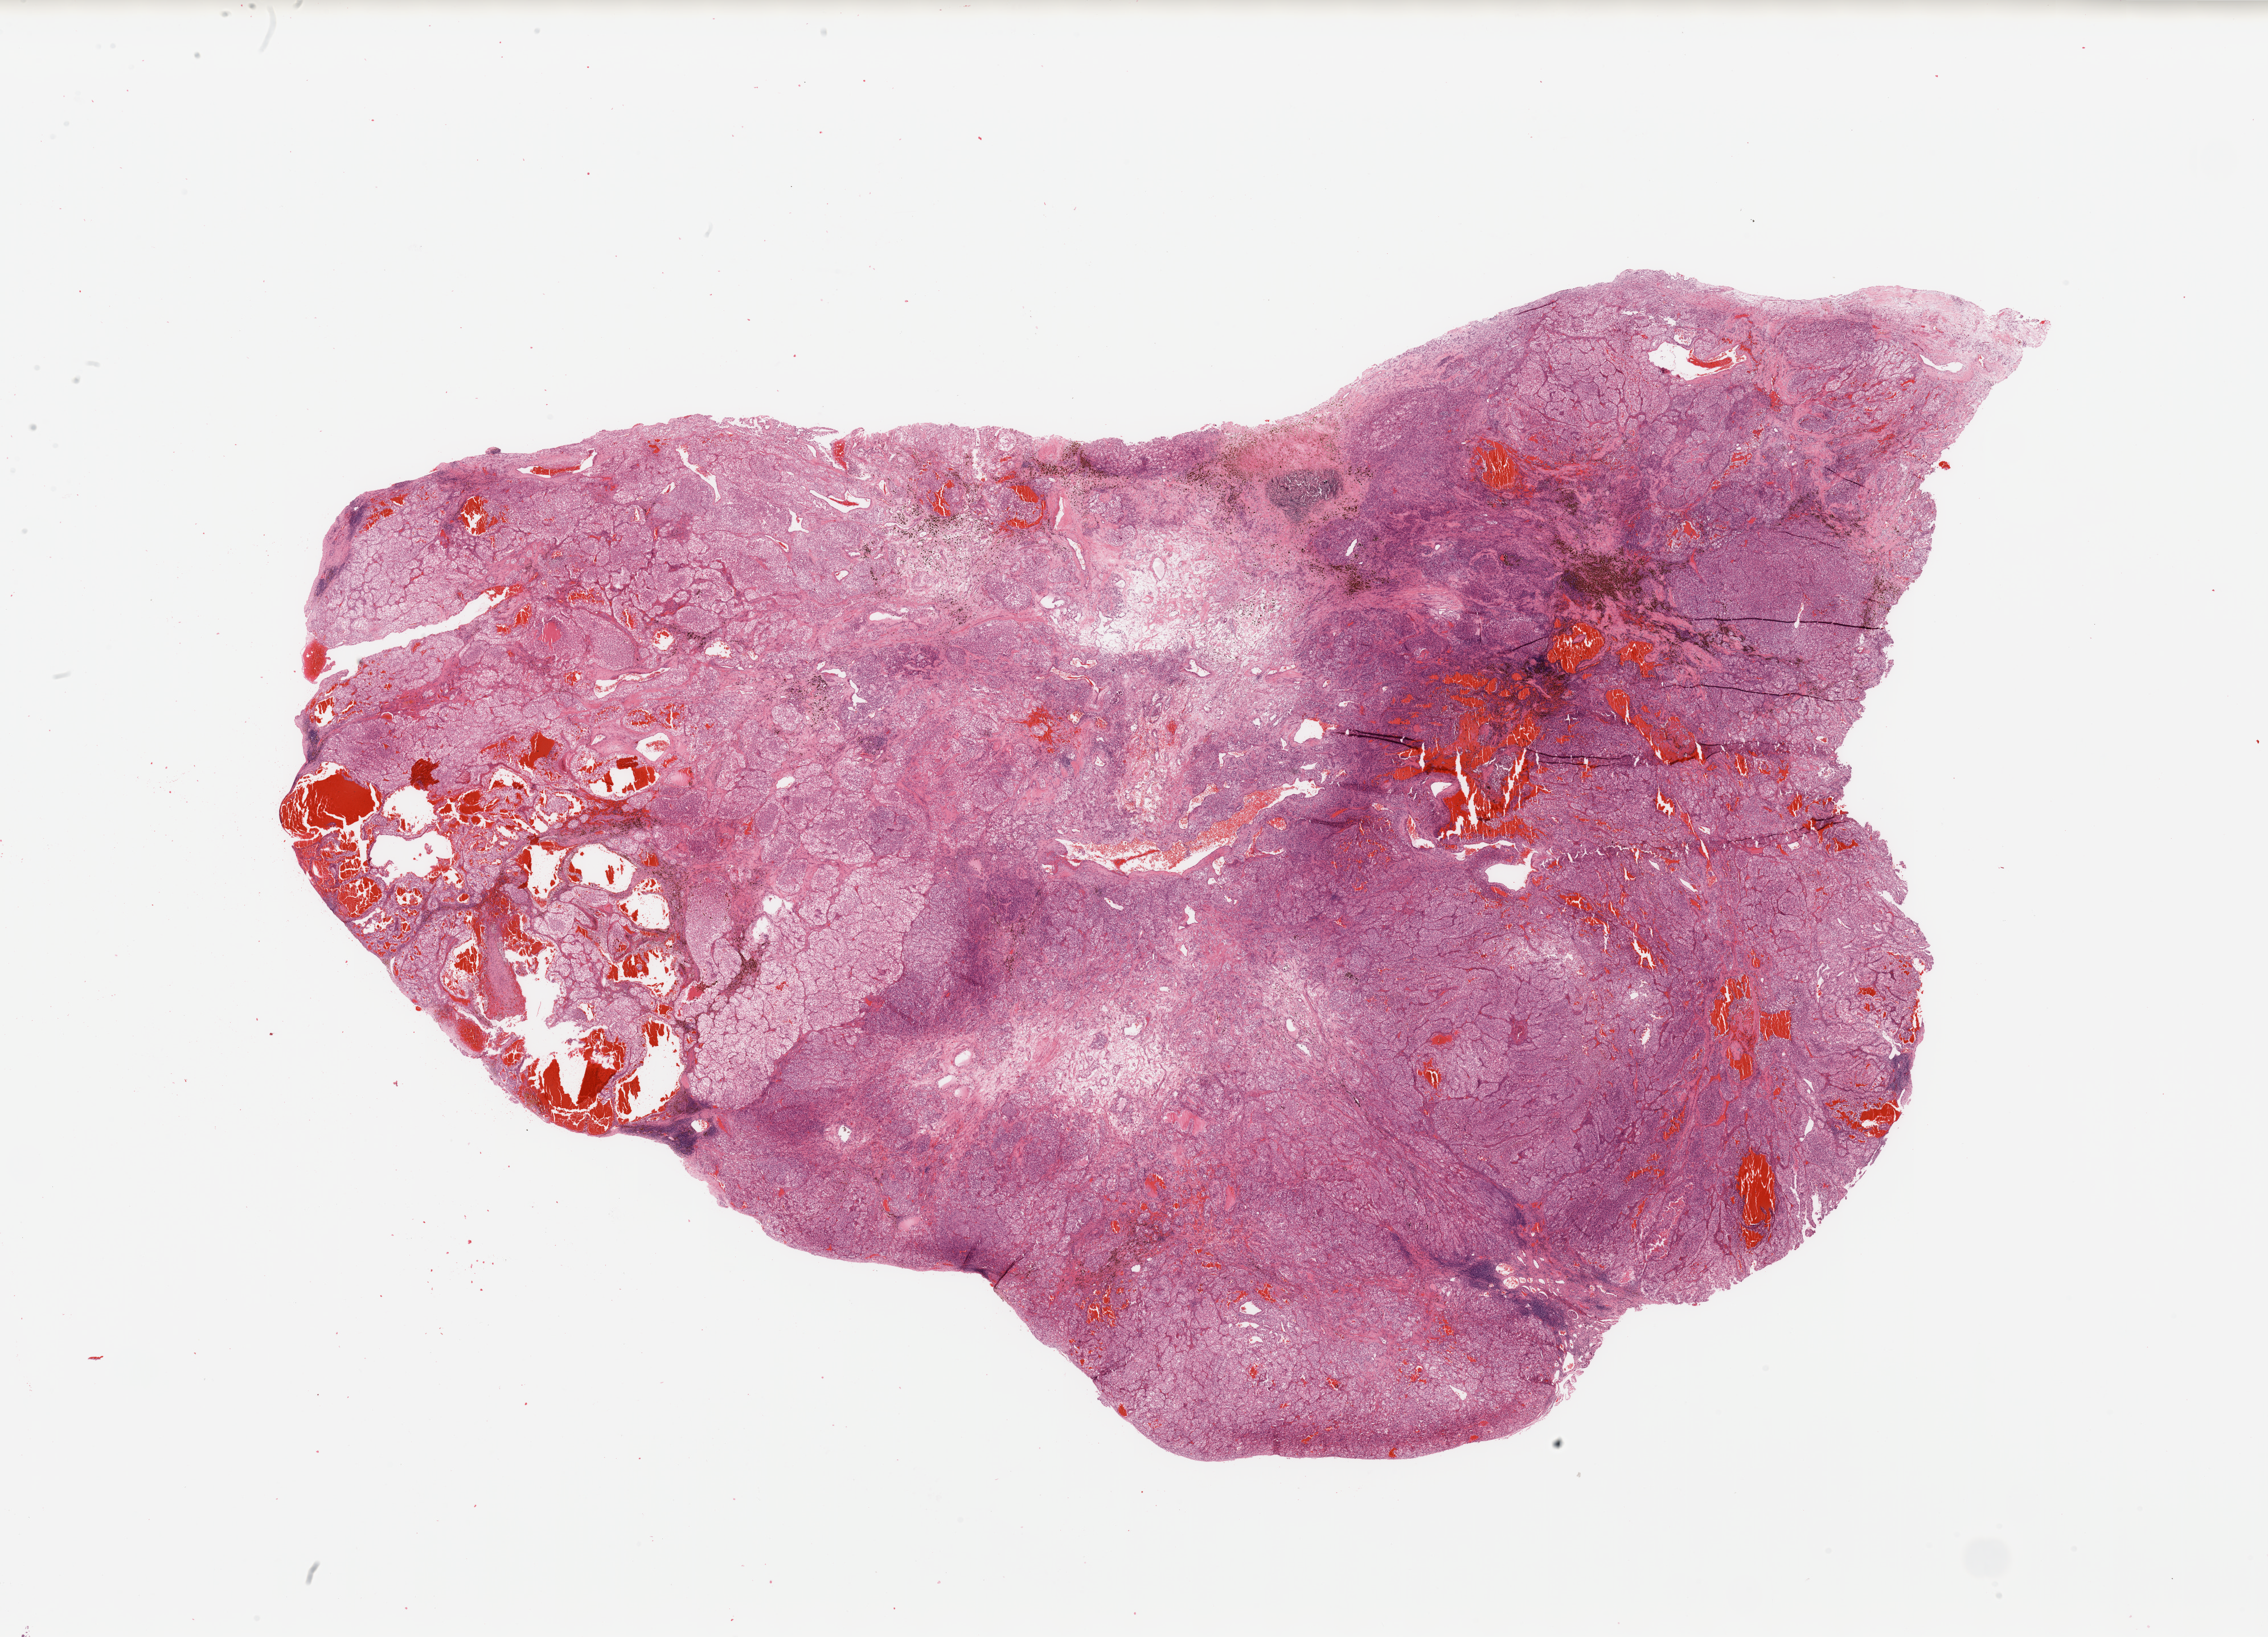
Hematoxylin and eosin (H&E) stained whole-slide image — low-resolution overview of the scanned area, about 31.5 x 22.7 mm (acquisition: 20x scan). Tumour tissue sample, sampled site: kidney. Patient: male, age 53 years. Histologic grade: G3 (poorly differentiated). Slide review estimates, as recorded: tumour nuclei 80%, necrosis 5%.
• diagnosis: Renal cell carcinoma, NOS